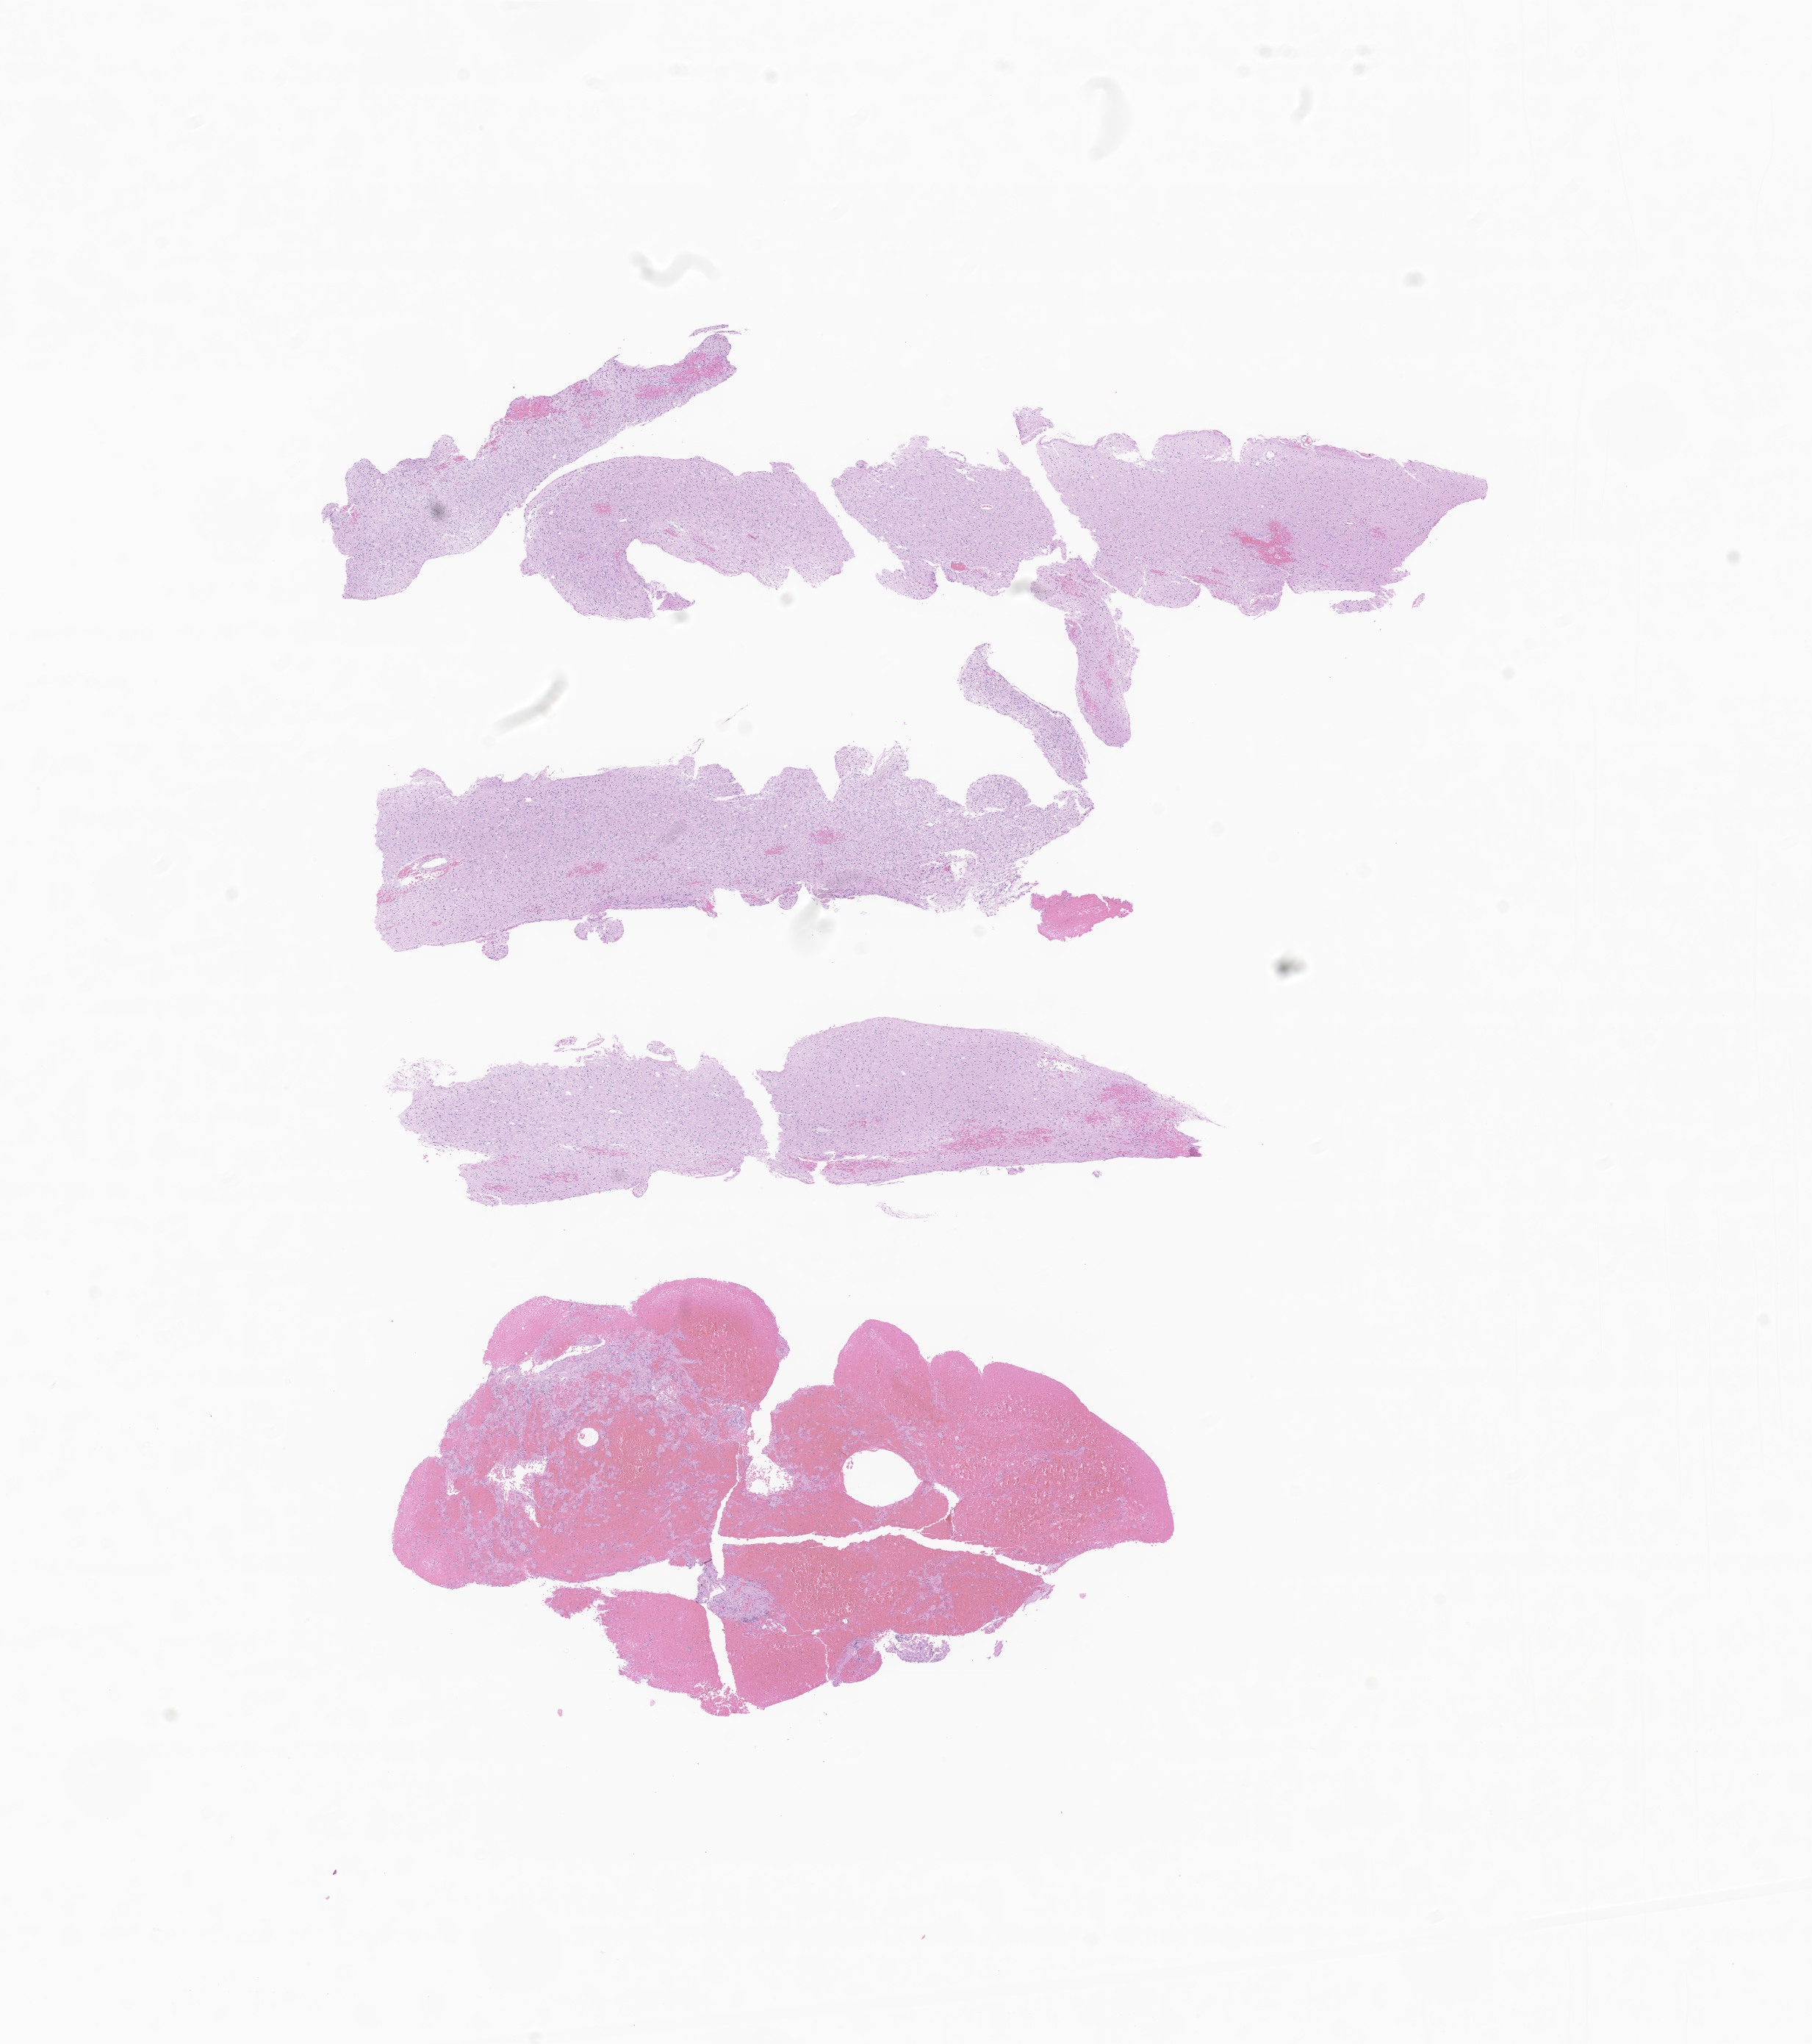
Whole-slide image, haematoxylin and eosin stain of tumor tissue from the brain — a low-resolution overview of the entire scanned area, about 10.4 x 11.7 mm. Formalin-fixed paraffin-embedded section. Male patient, age 123 months (10 years 3 months).
Diagnosis (ICD-O-3 morphology term): Glioma, malignant.